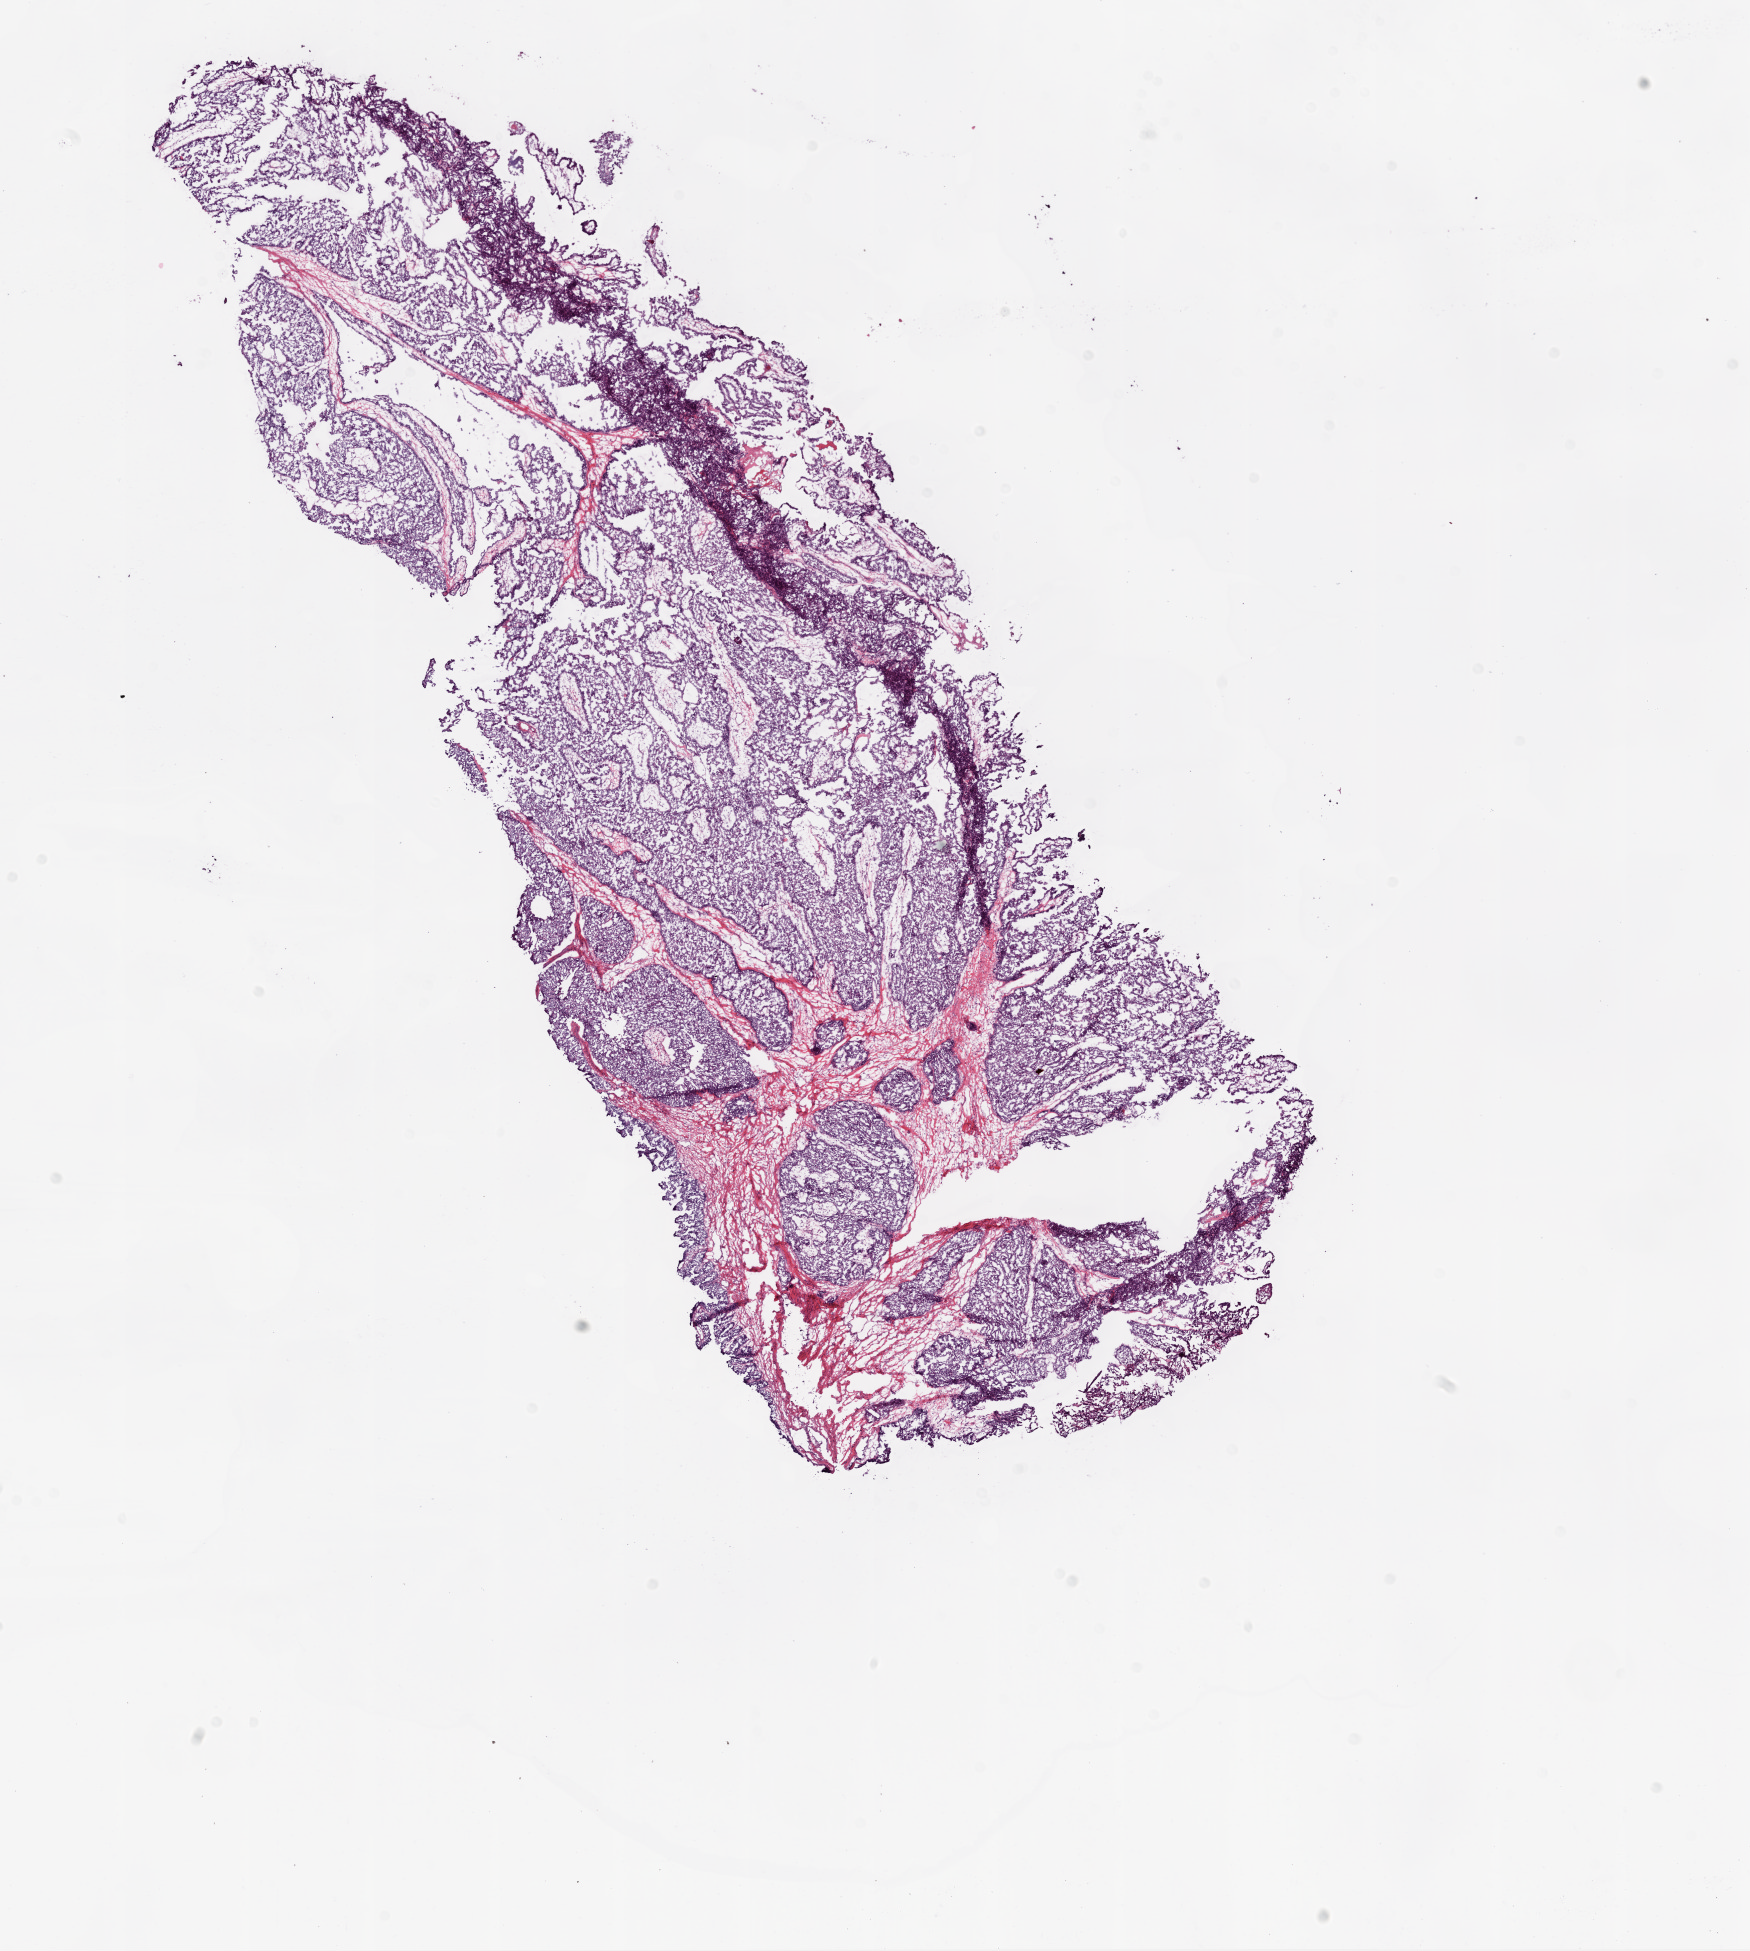
H&E whole-slide image — whole scanned area (about 14.0 x 15.7 mm) shown as a low-resolution overview, frozen section from the bottom of the tissue portion, sample: primary tumour, ovary. Female patient; age at initial diagnosis 56 years. Histologic grade: G3 (poorly differentiated). Composition of this section per pathologist review: tumour cells 80%, tumour nuclei 90%, normal cells 0%, stromal cells 20%, necrosis 0%.
• histologic diagnosis: Serous cystadenocarcinoma, NOS